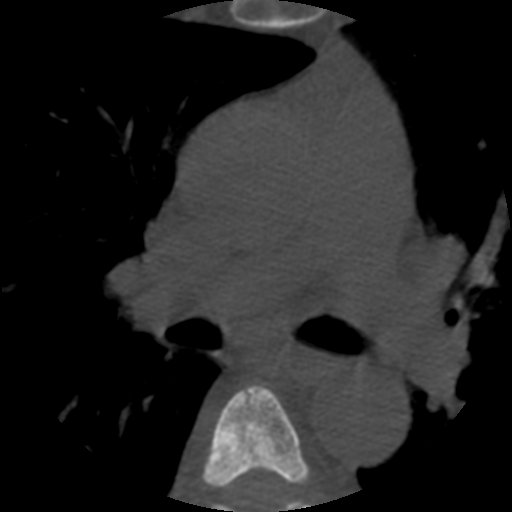
CT including the spine, one axial slice. Position 372 of 508 along the scan axis. Reconstruction kernel STANDARD. 120 kVp. Bone window (W 1800 / L 400 HU). 1.25 mm slice thickness. 512 × 512 image matrix. Patient age 57 years. From the clinical record (not read from this slice): primary cancer: prostate.
Outlined on this slice (semi-automatically segmented with operator editing):
- T5 vertebra: box from (x=202, y=386) to (x=310, y=508) px
- T6 vertebra: (x=211, y=500)–(x=310, y=512)